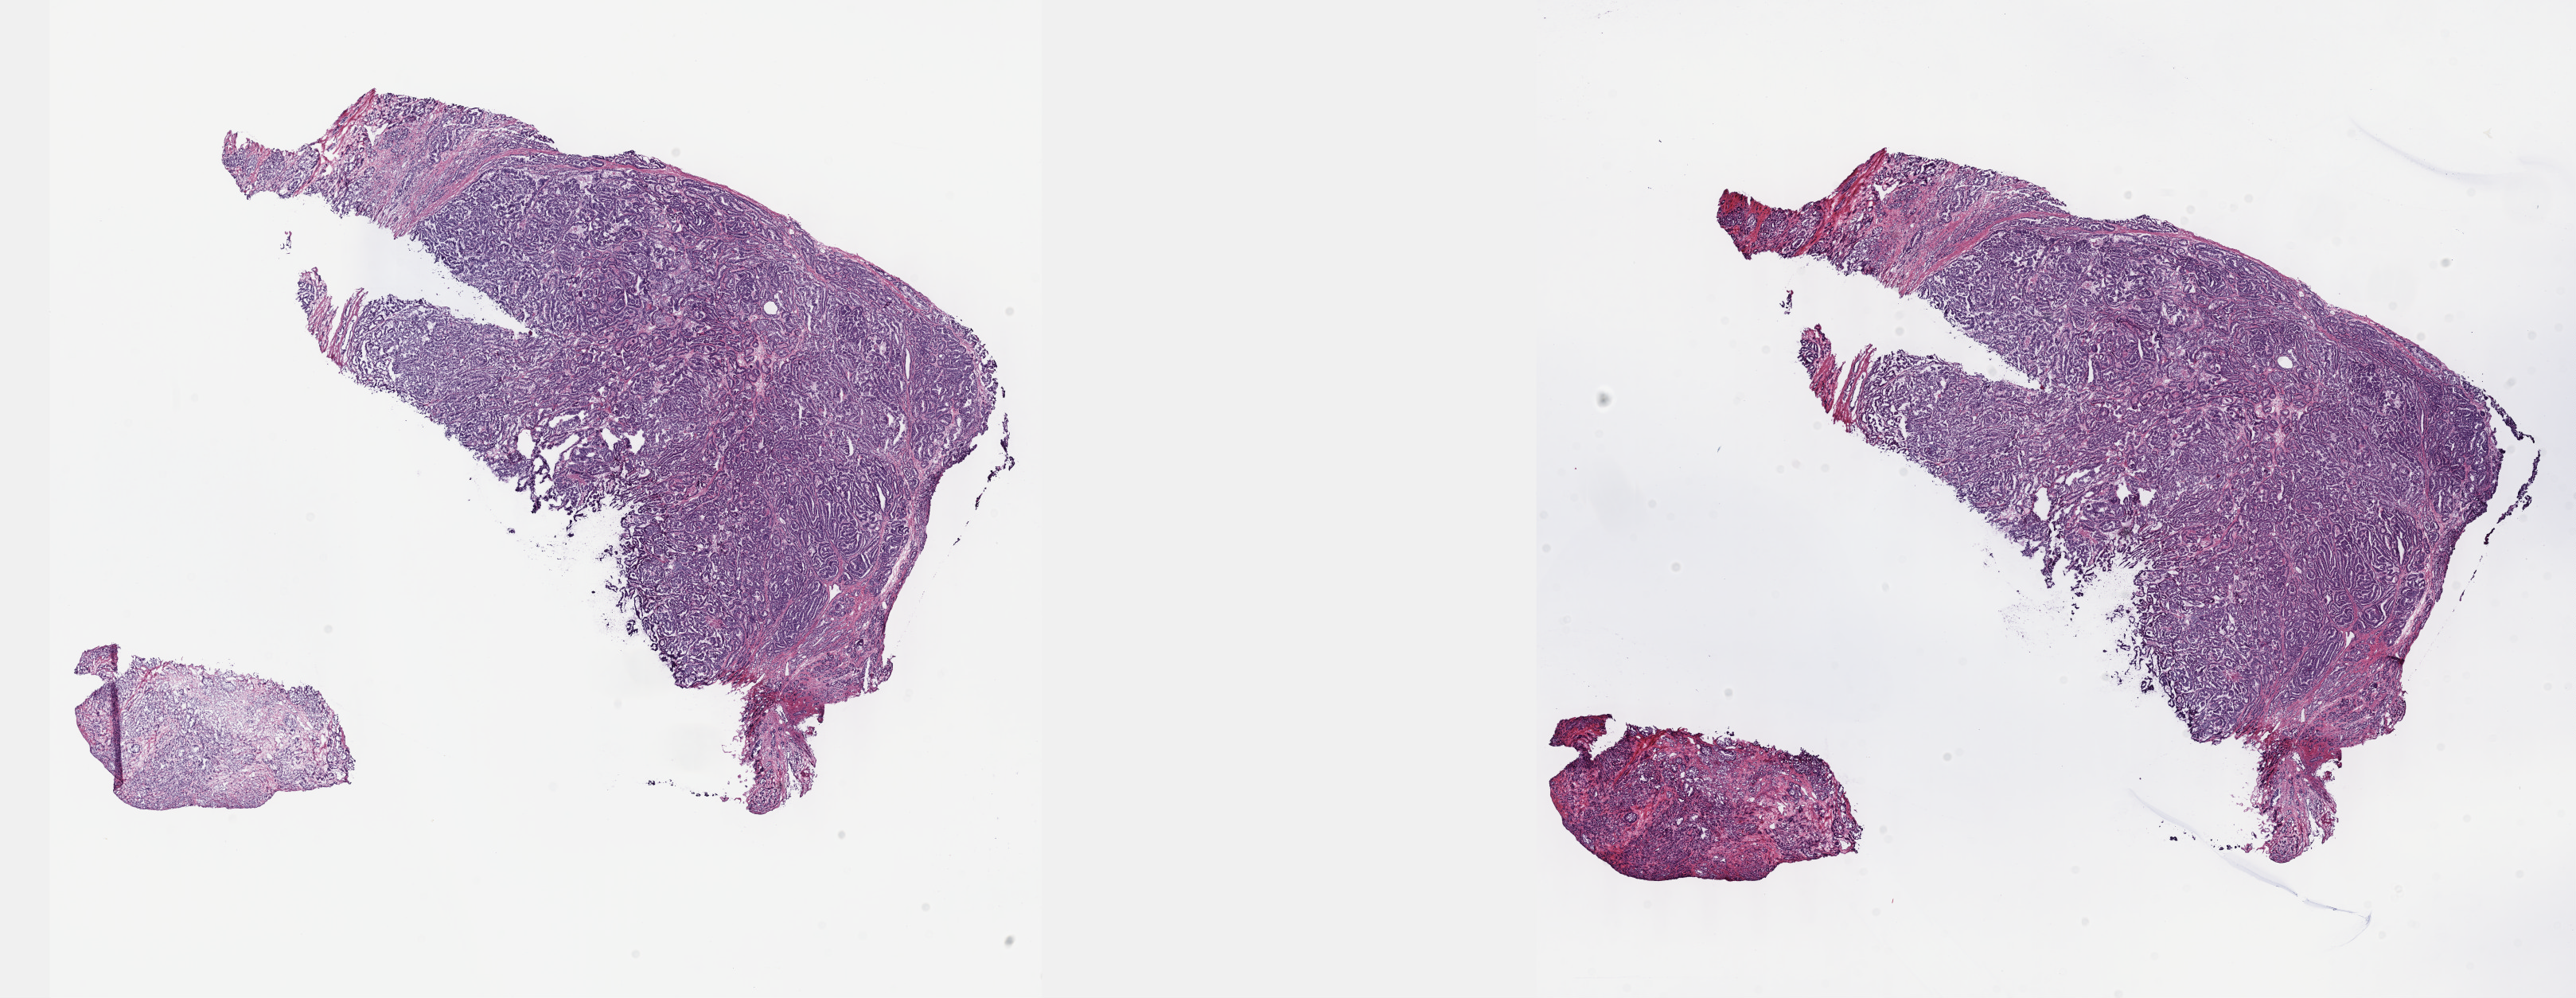
Whole-slide histology image, H&E, whole scanned area (about 26.2 x 10.1 mm) shown as a low-resolution overview, frozen section from the top of the tissue portion, primary tumour sample from the prostate. Patient: male, age at initial diagnosis 63 years. Slide review estimates, as recorded: tumour cells 85%, tumour nuclei 90%.
Pathologic diagnosis: Adenocarcinoma, NOS.